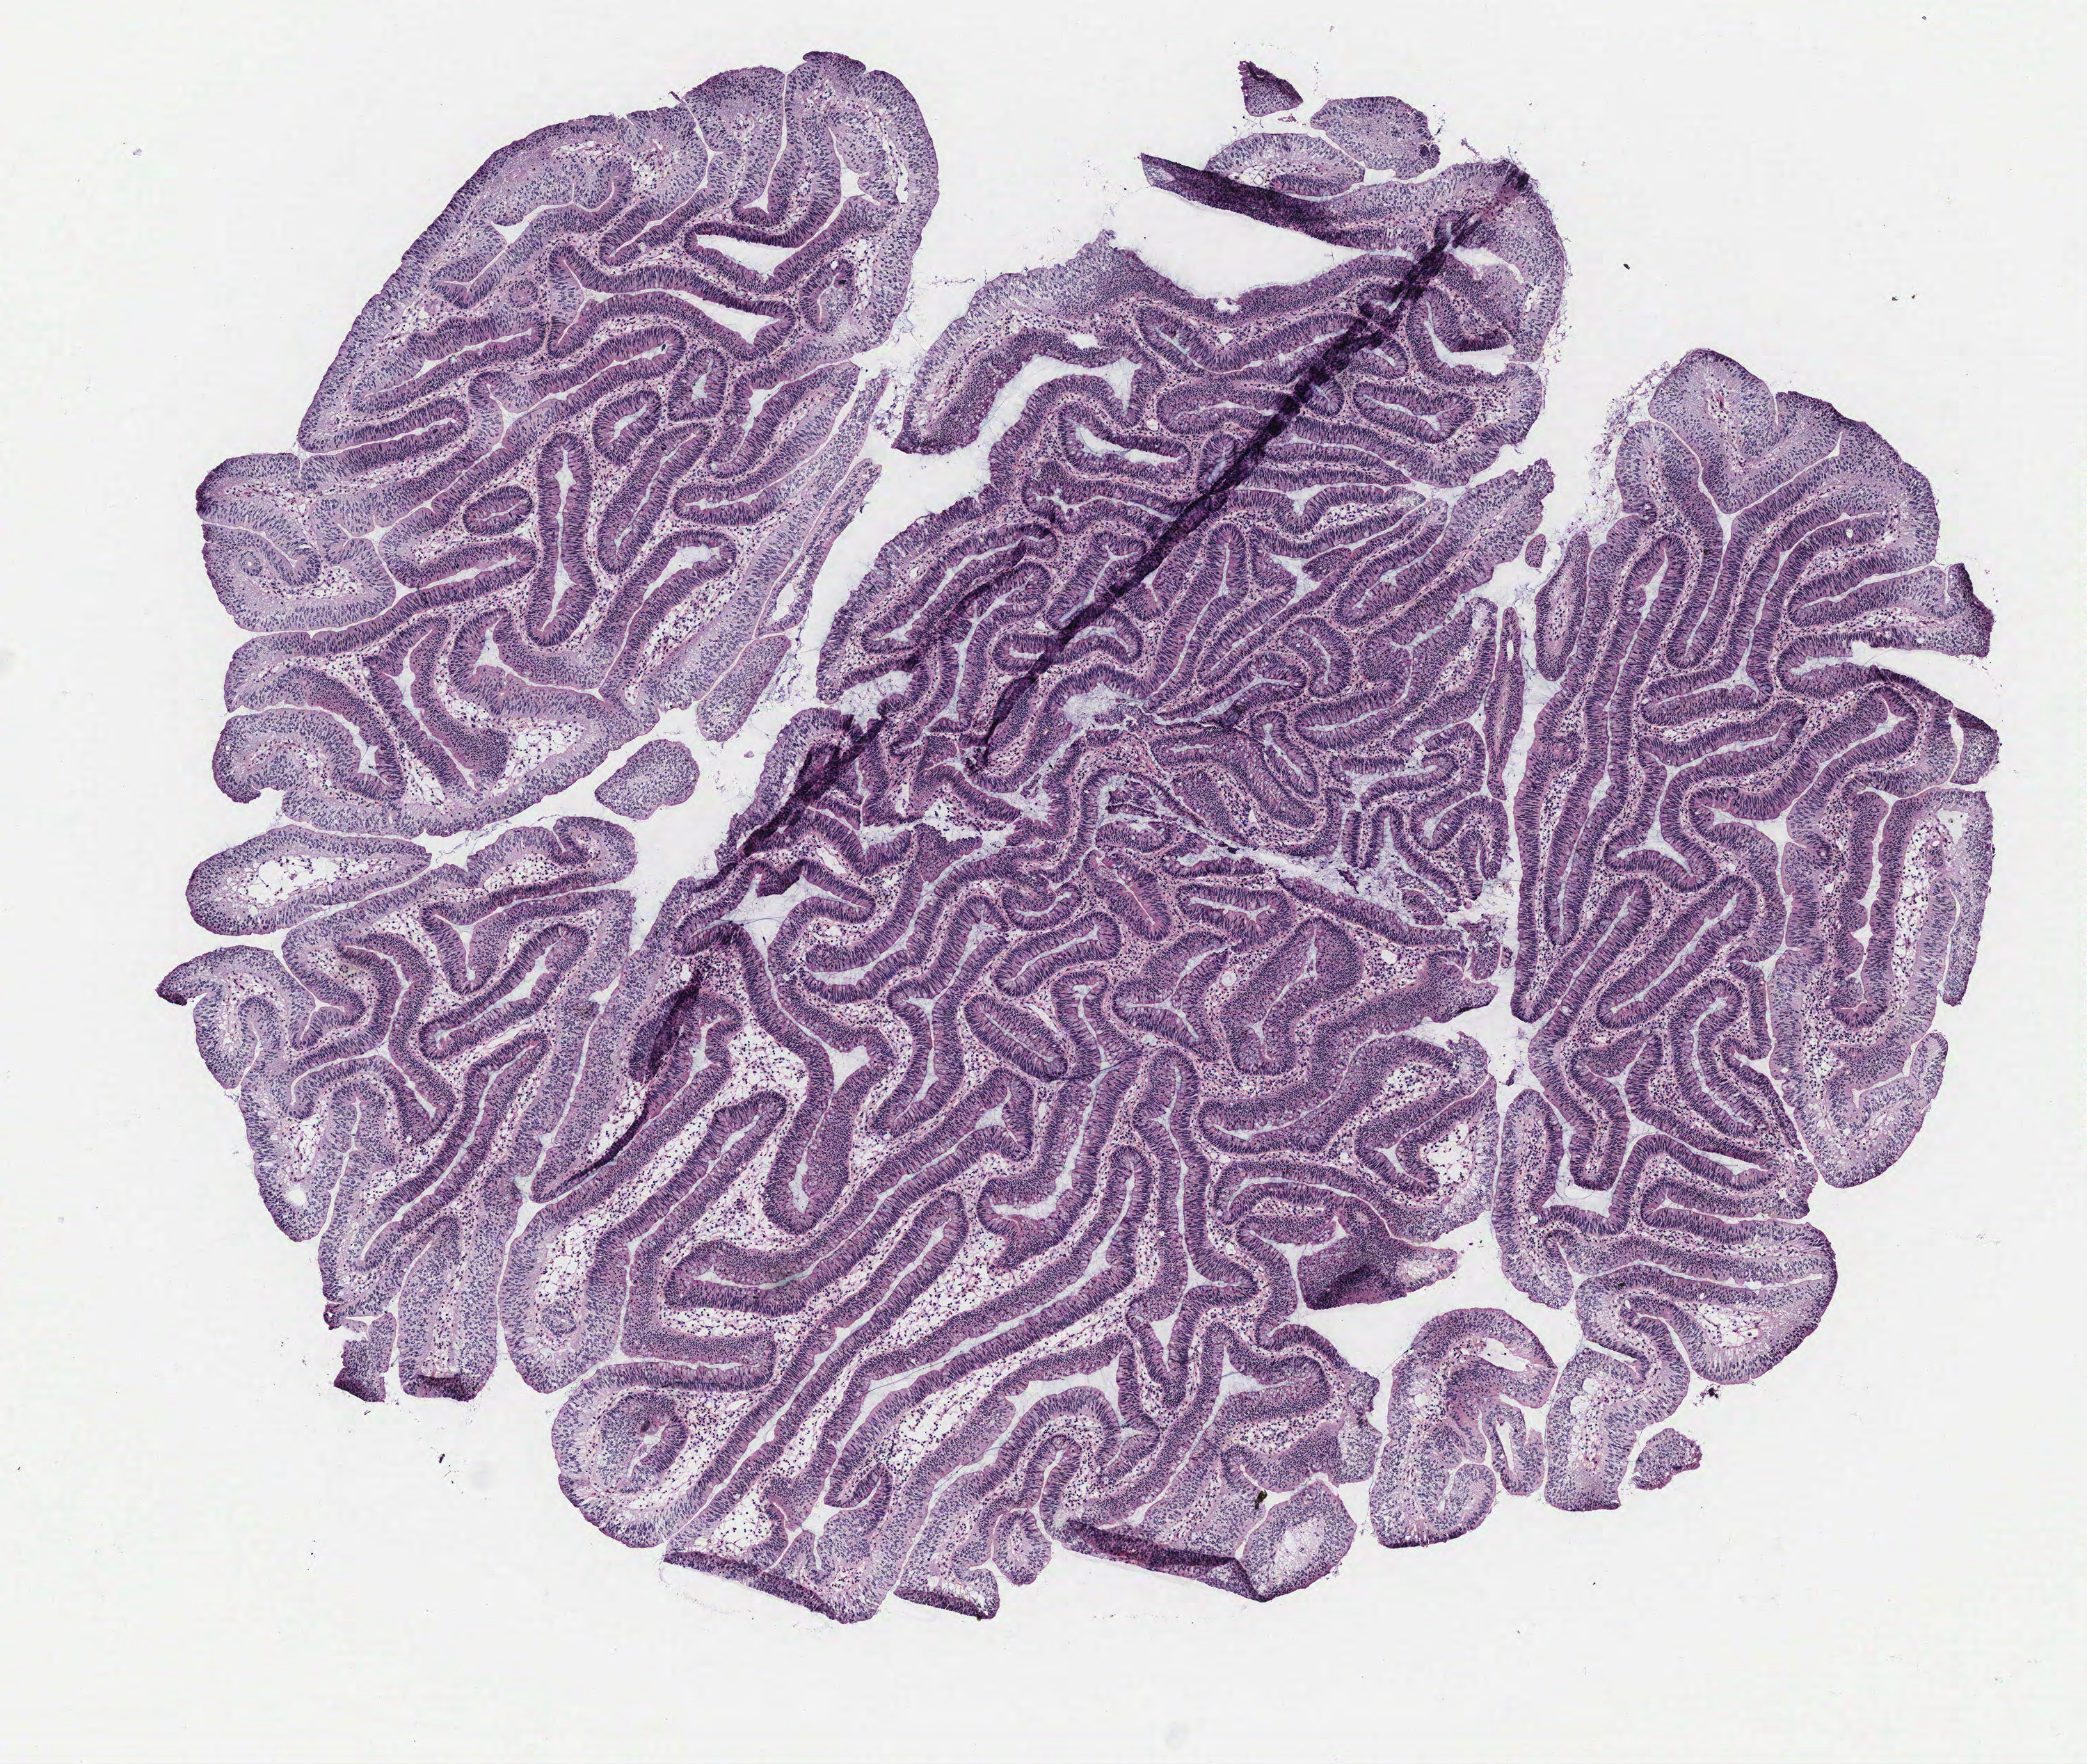
Whole-slide histology image, Hematoxylin and eosin (H&E) stained, a low-resolution overview of the entire scanned area, about 6.0 x 5.1 mm (acquisition: 40x scan). Colon, tissue type not recorded. Patient sex: female.
• patient diagnosis: Adenocarcinoma, NOS